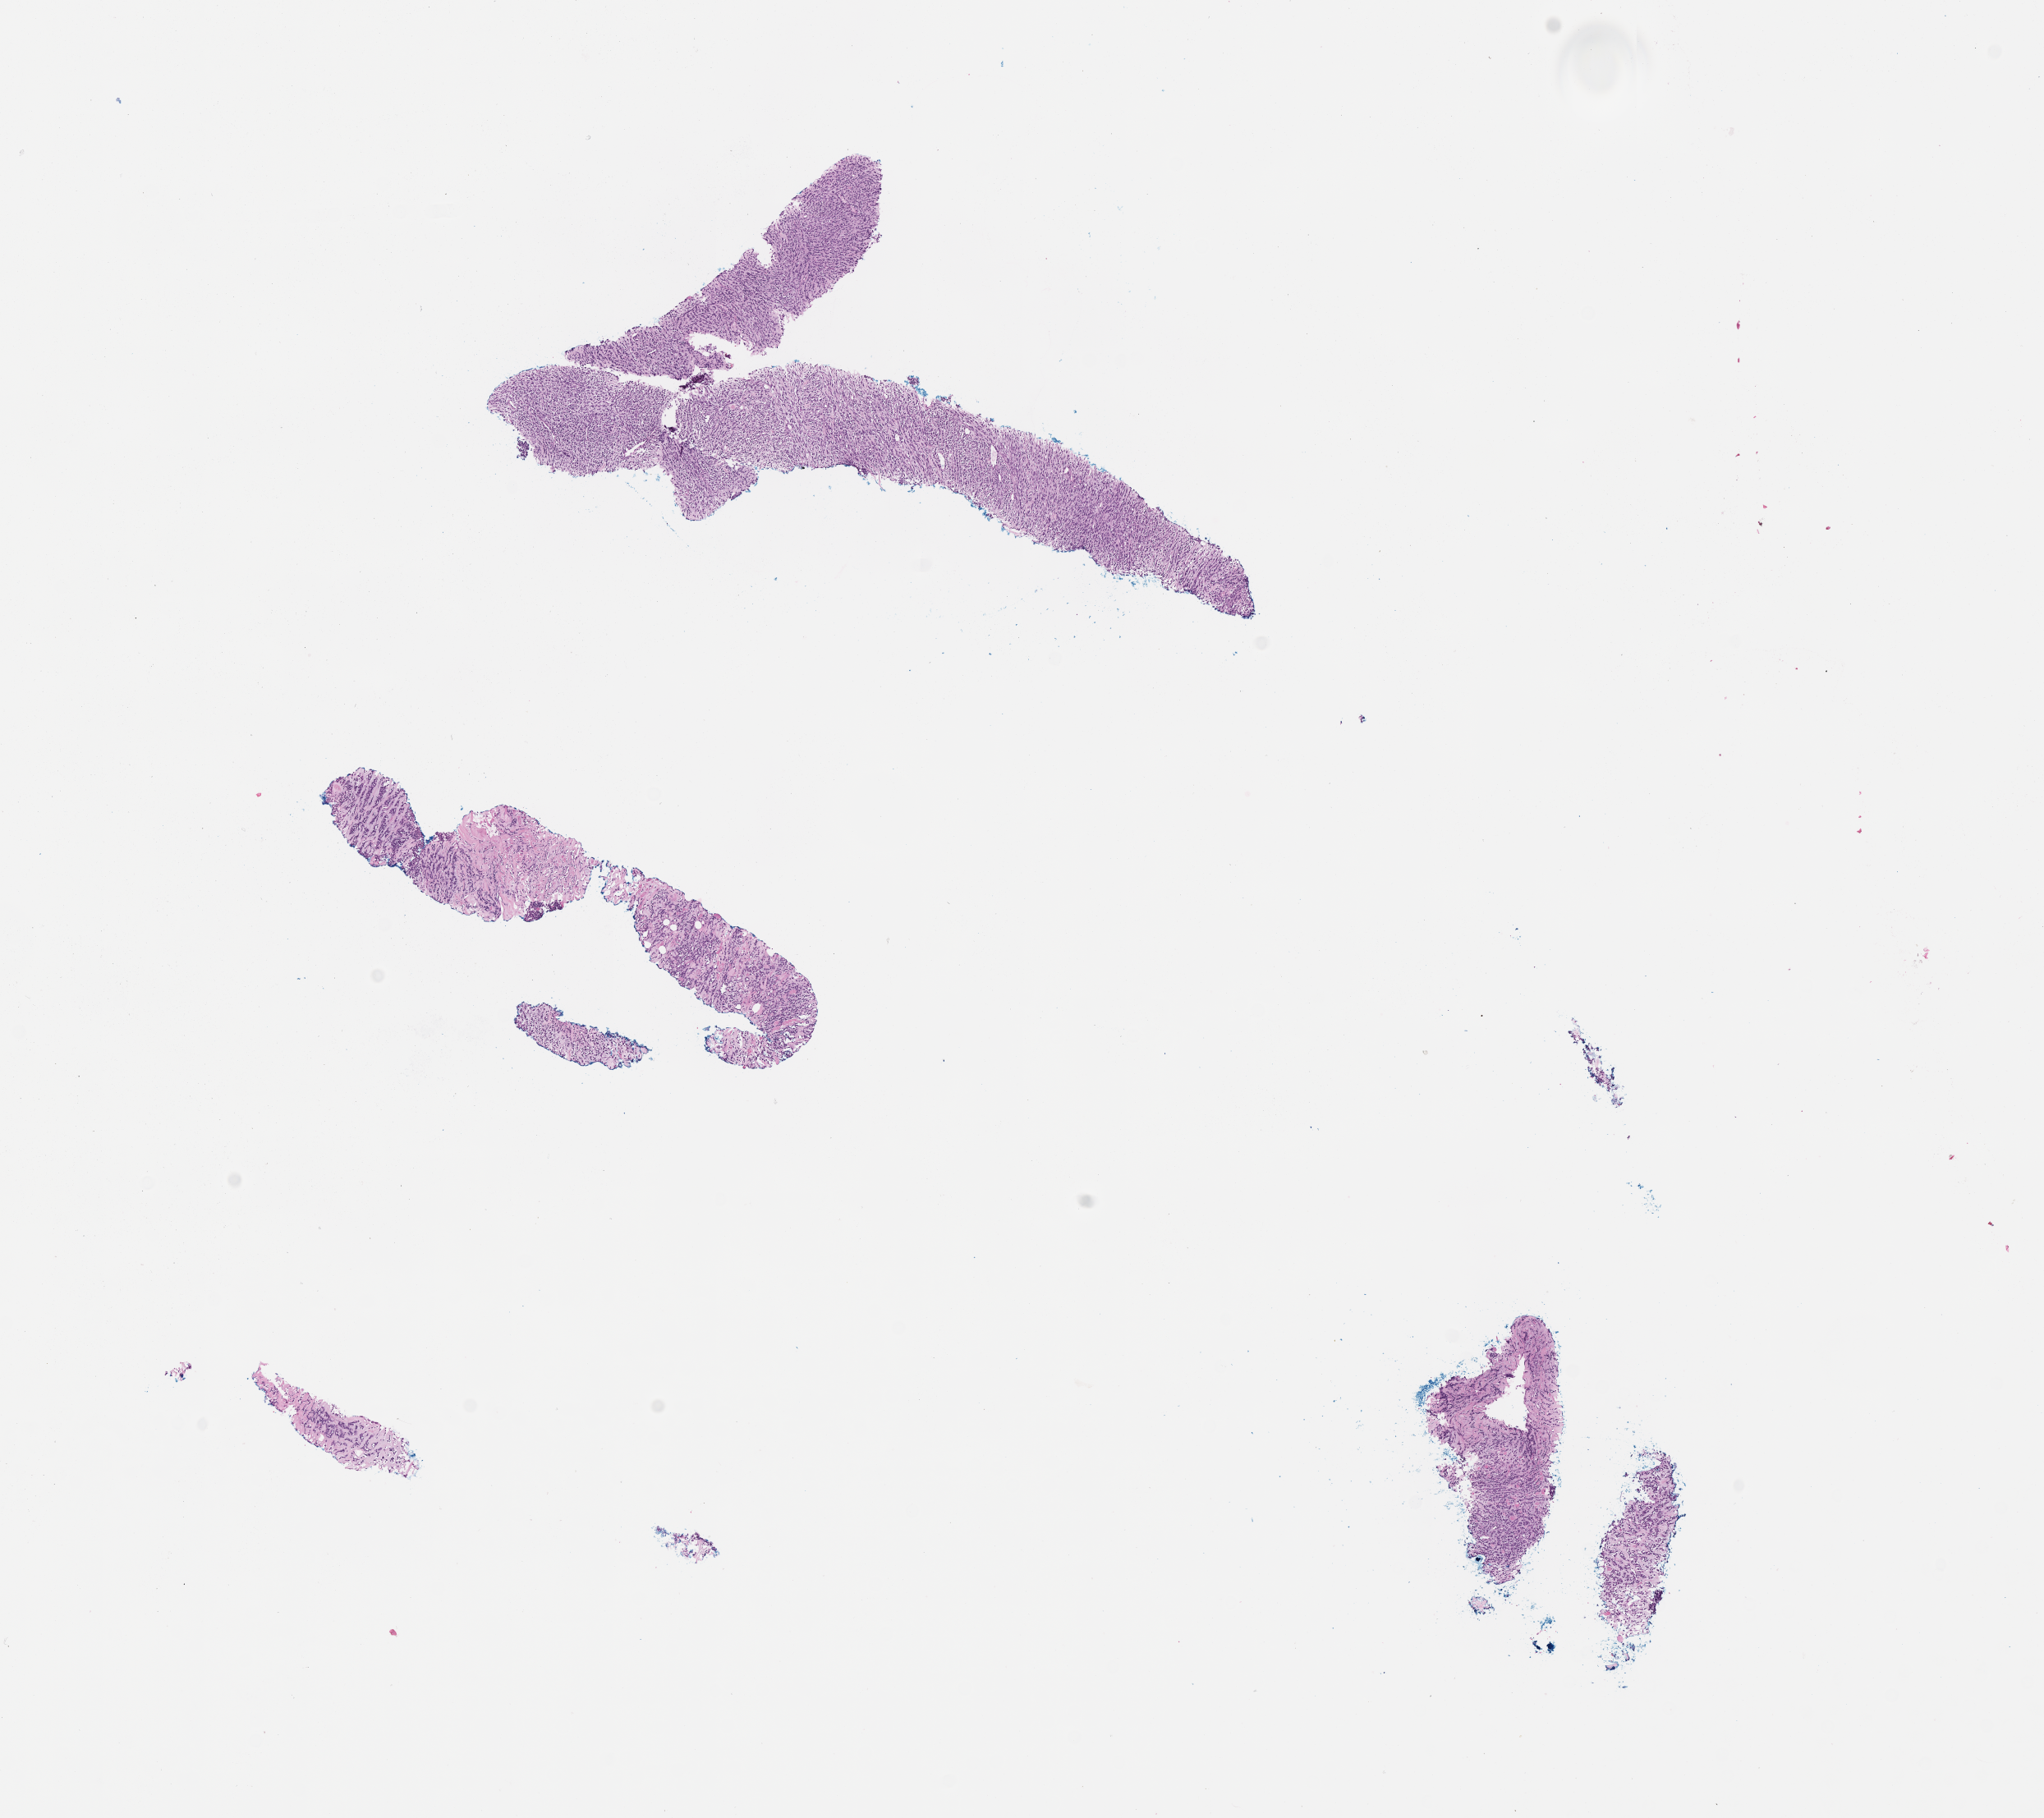
Digitized haematoxylin and eosin-stained section of tumor tissue — shown as a low-resolution overview of the whole scanned area (about 10.1 x 9.0 mm); formalin-fixed, paraffin-embedded (FFPE) tissue; sample anatomic site: soft tissue, mandible-right. Male patient, age at diagnosis 17.1 years.
Primary site (case record): infratemporal fossa (PM). Stage (as recorded): 4. Diagnosis: rhabdomyosarcoma; histological classification: embryonal rhabdomyosarcoma.